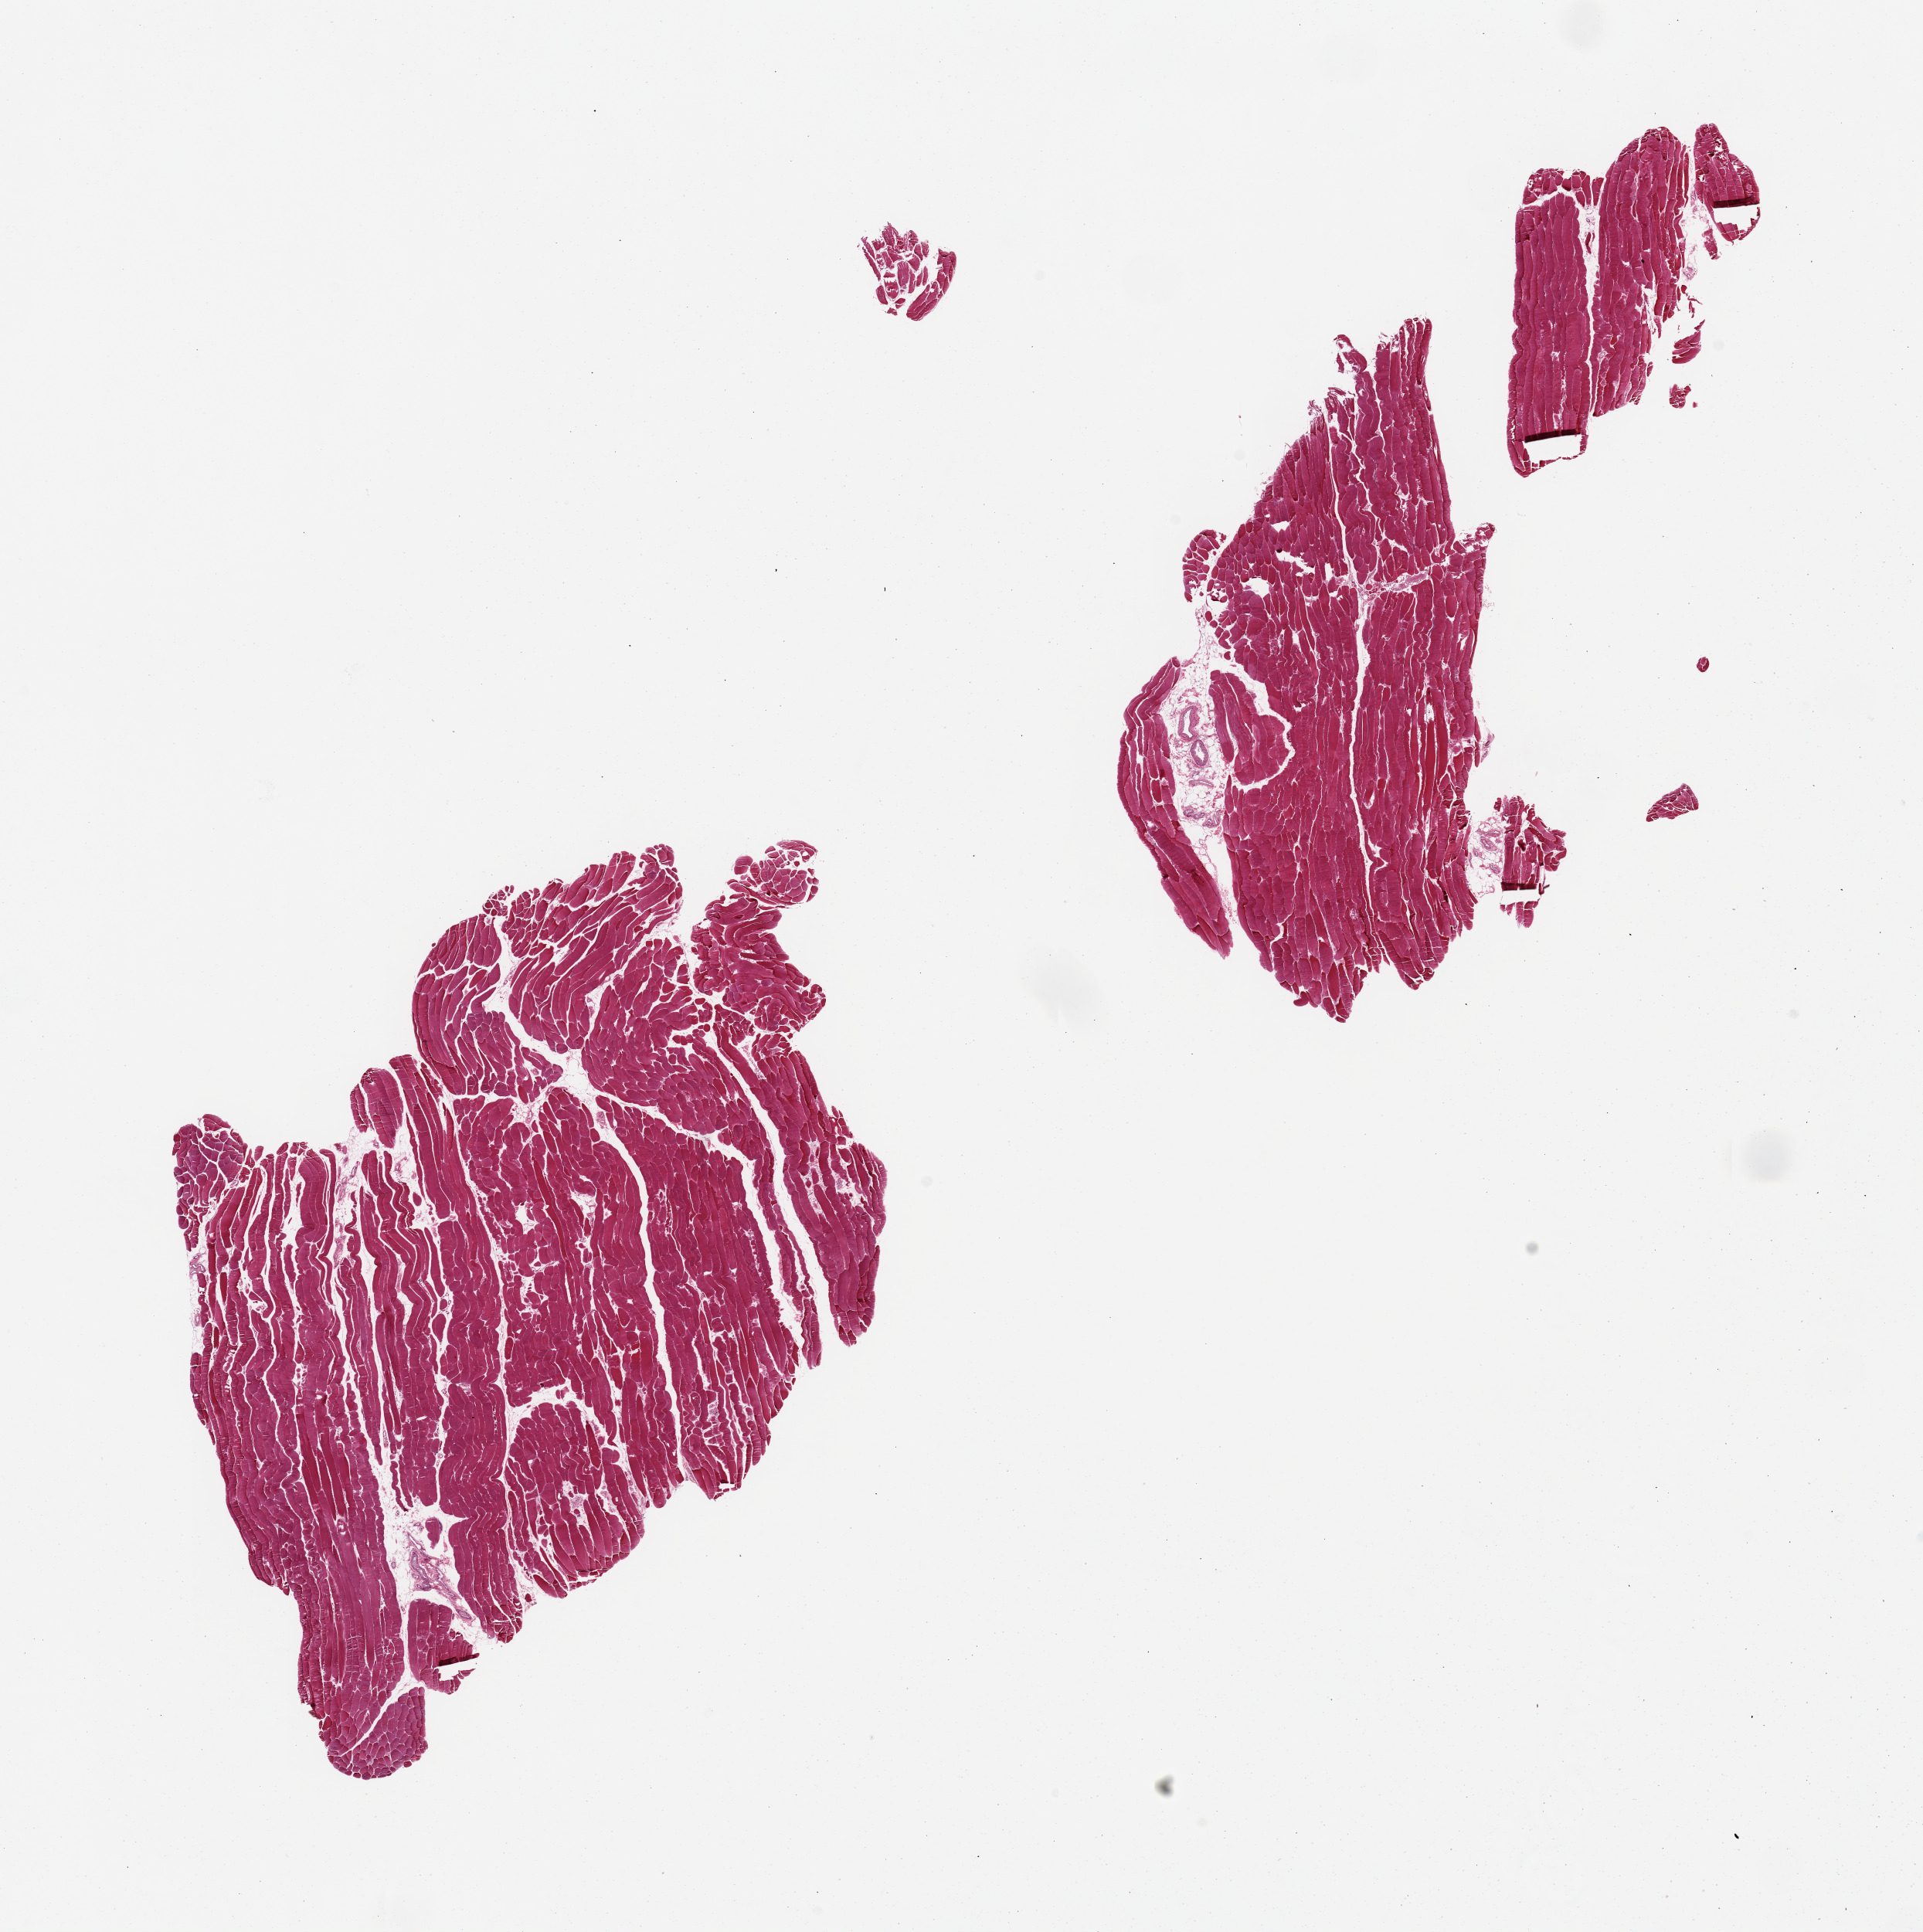
Haematoxylin and eosin whole-slide image, shown as a low-resolution overview of the whole scanned area (about 19.7 x 19.8 mm, acquisition: 20x scan). PAXgene-fixed, paraffin-embedded tissue. Section of skeletal muscle (target tissue). Donor tissue sample. Male donor.
Review note (as recorded): 2 pieces, minimal (~5%) interstitial fat.